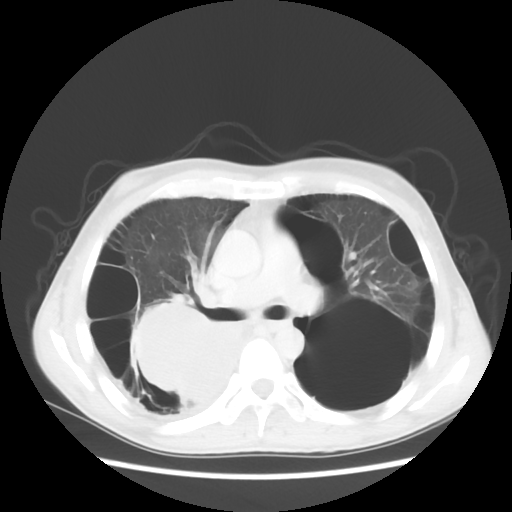
Chest CT, one axial slice. Position 33 of 56 along the scan axis. Reconstruction kernel STANDARD. 140 kVp. Lung window (W 1500 / L -600 HU). 512 × 512 image matrix. Male patient, age 41 years. Case-level facts recorded for this patient, not image findings: clinical TNM (as recorded): T4 N0 M1a.
Annotated regions visible in this slice (rectangle marked by the reading radiologist):
- lung tumour (recorded histology: large cell carcinoma): bounding box <137,301,244,408> (left, top, right, bottom; pixels)